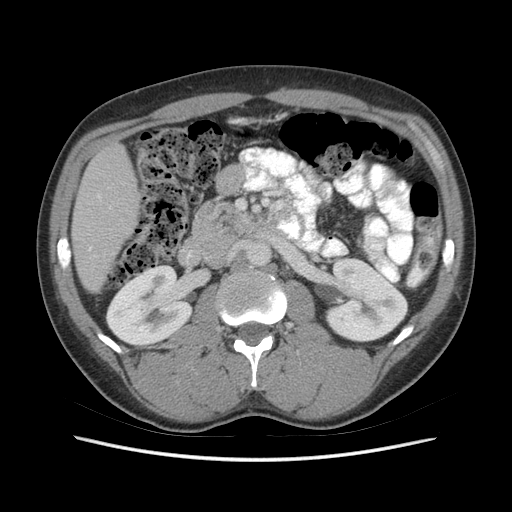
Contrast-enhanced abdominal CT (liver protocol), one axial slice; slice 18 of 73 in the series (ordered by position); reconstruction kernel STANDARD; 140 kVp; soft-tissue window (W 400 / L 40 HU); 2.5 mm slice thickness; 512 × 512 image matrix, field of view 360 × 360 mm. From the clinical record (not read from this slice): diagnosis: hepatocellular carcinoma (patient treated with transarterial chemoembolisation; whether this scan precedes or follows treatment is not stated here); TNM stage (as recorded): Stage-IIIA; Child-Pugh class: A.
Structures marked on this image (semi-automatically segmented with operator editing):
- liver parenchyma outside the tumour (the mass and vessels are separate outlines, so this box may not span the whole liver): bounding box <72,142,140,292> (left, top, right, bottom; pixels)
- liver vessels: <89,248,91,250>